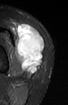
MRI of an extremity soft-tissue mass, one axial slice. Position 30 of 52 along the scan axis. STIR. MR volume resampled by the dataset authors to the PET/CT grid (not the native acquisition matrix). 68 × 105 image matrix. Female patient. Case-level facts recorded for this patient, not image findings: histological type: spindle cell suggestive of biphasic synovial sarcoma; grade: intermediate; site of the primary tumour: left knee.
Annotated regions visible in this slice (expert contour drawn on MRI and transferred to this co-registered scan by the dataset authors):
- gross tumour volume including surrounding oedema: bounding box (x1, y1, x2, y2) in pixels: (14, 22, 43, 74)
- gross tumour volume (mass): (15, 25, 43, 74)